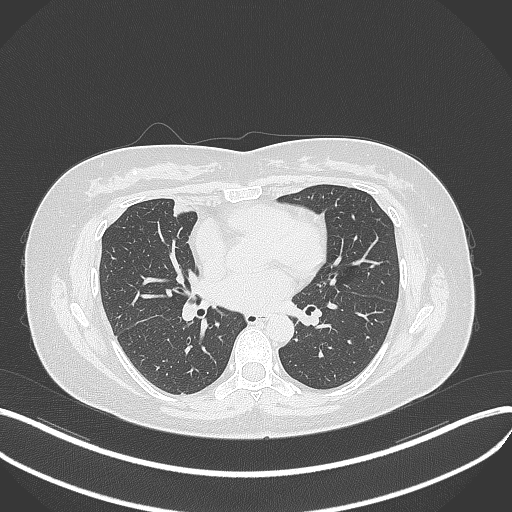
Chest CT, one axial slice. Slice 151 of 273 in the series (ordered by position). Lung window (W 1500 / L -600 HU). 512 × 512 image matrix, field of view 400 × 400 mm. Female patient, age 42 years. Case-level facts recorded for this patient, not image findings: clinical TNM (as recorded): T1b N0 M0.
Annotated regions visible in this slice (rectangle marked by the reading radiologist):
- lung tumour (recorded histology: adenocarcinoma): box from (x=169, y=193) to (x=195, y=222) px